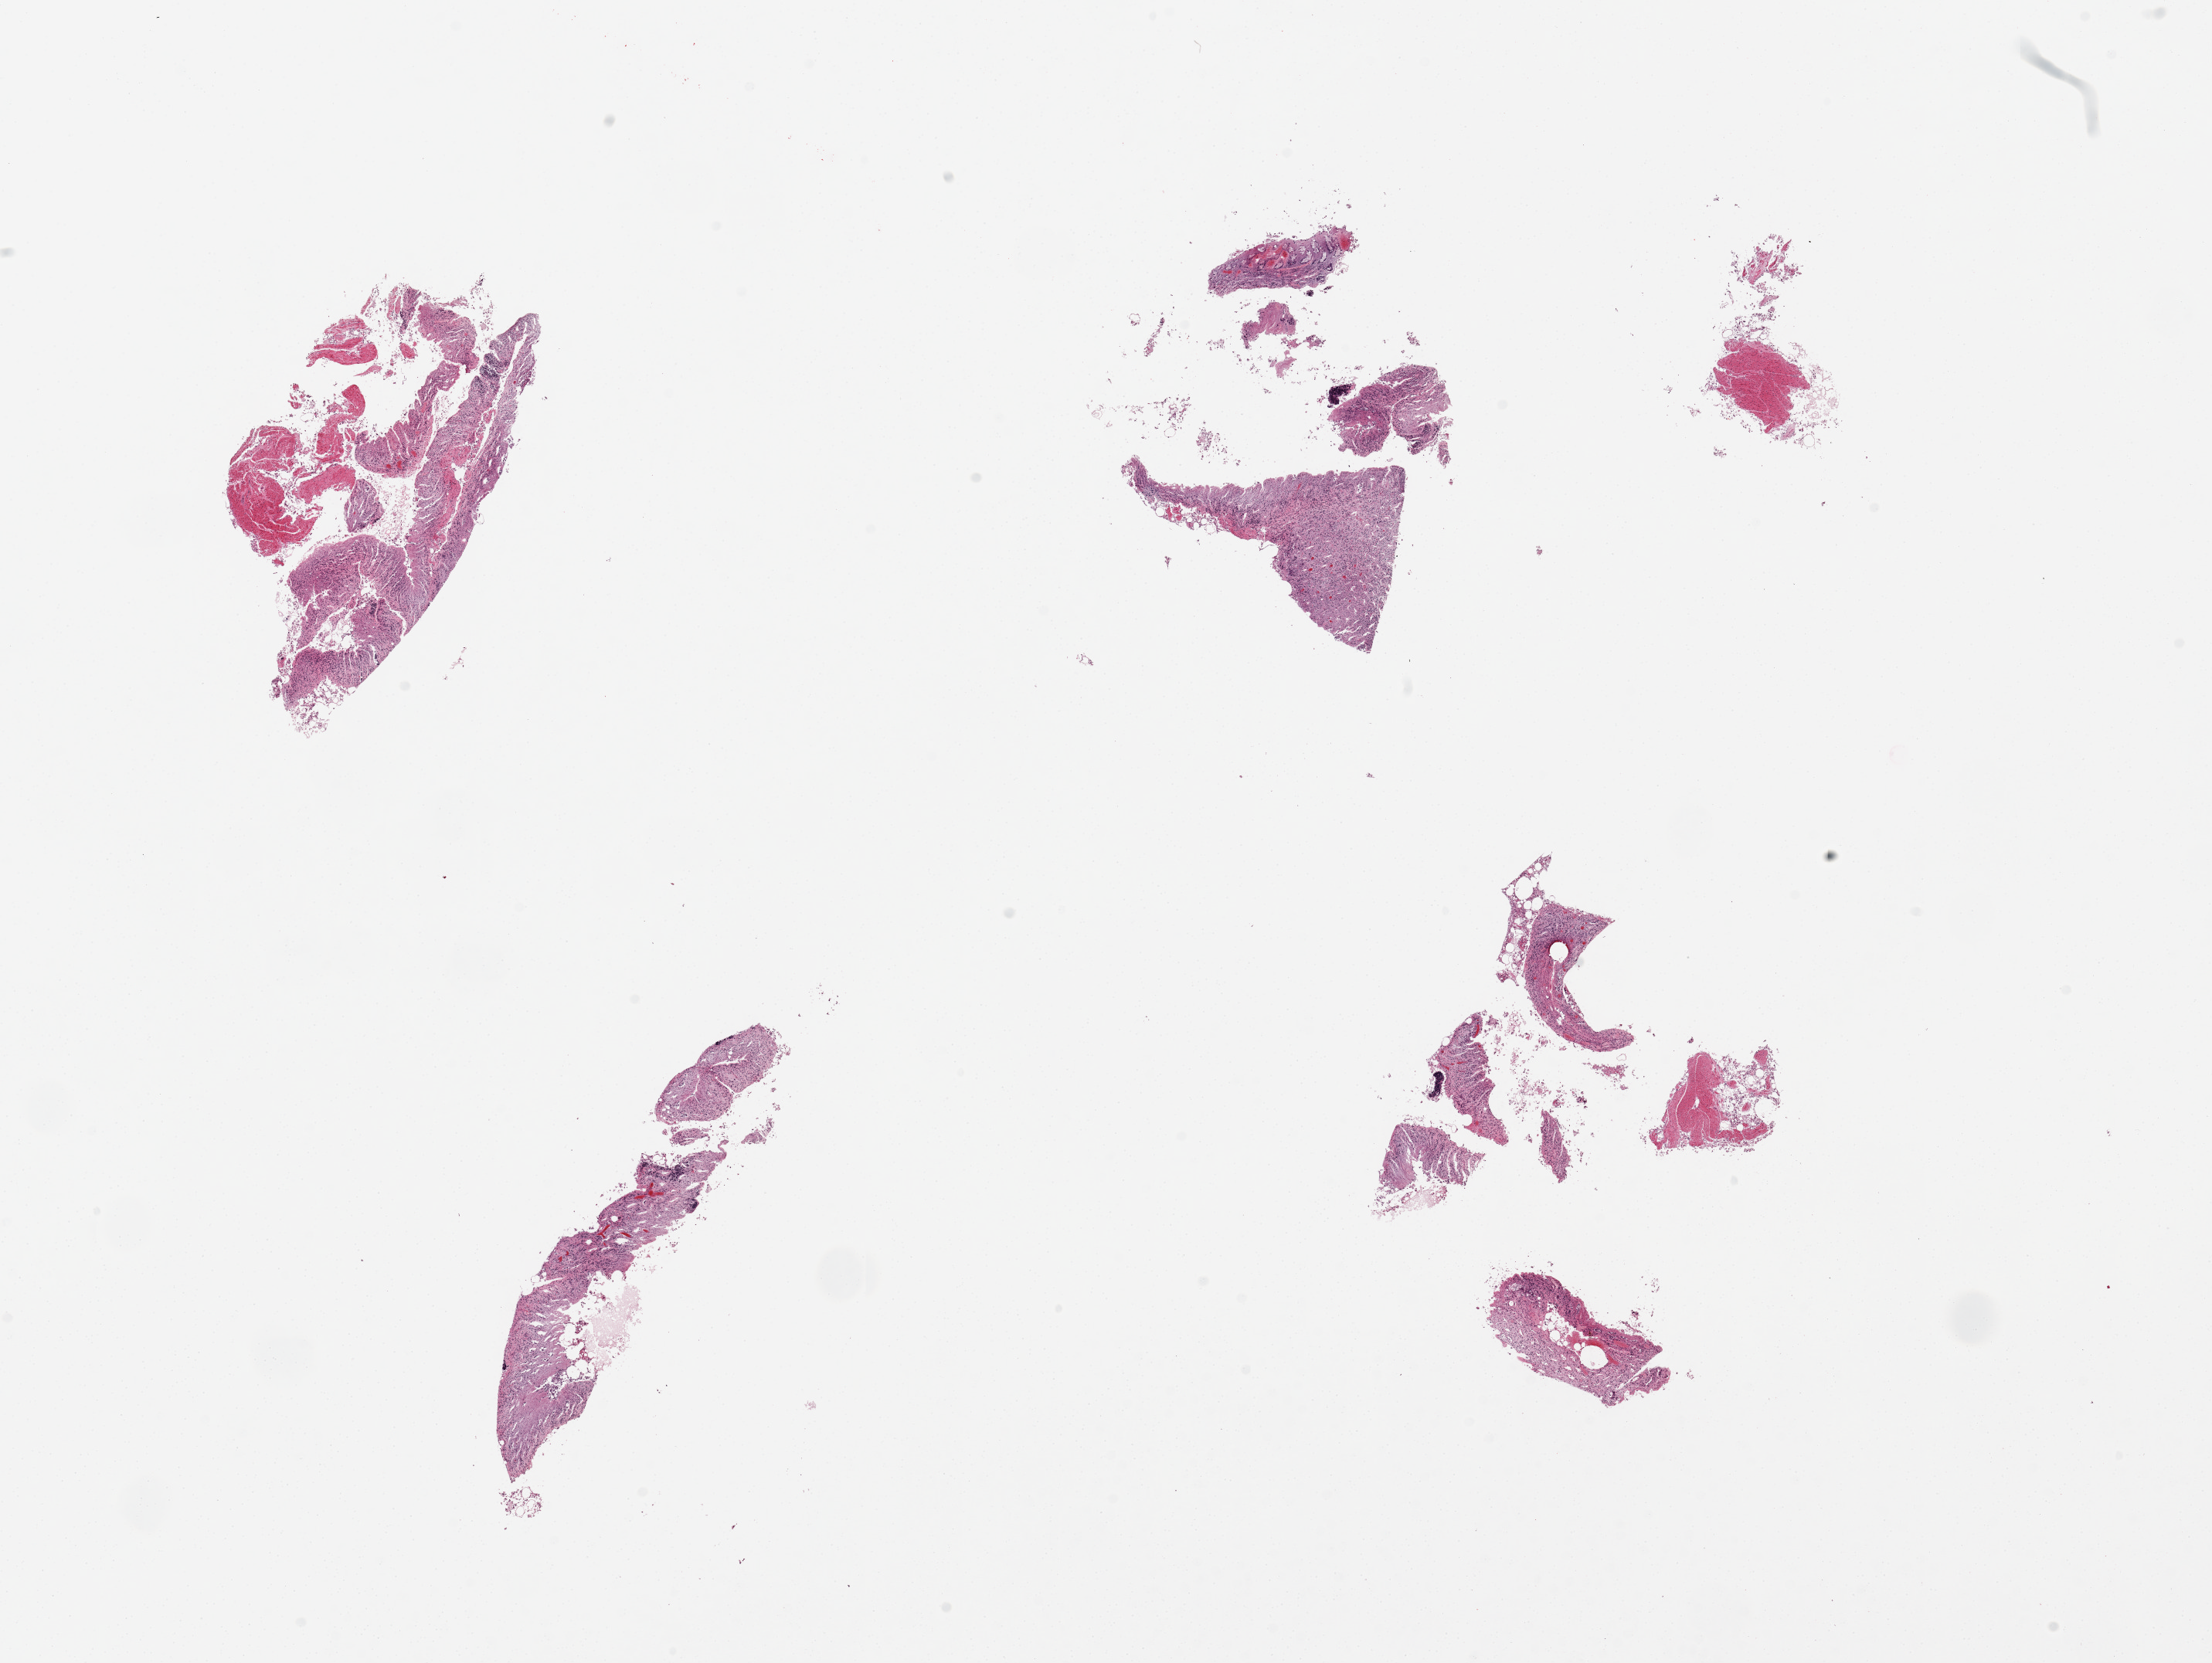
Digitized hematoxylin and eosin (H&E)-stained section, a low-resolution overview of the entire scanned area, about 22.6 x 17.0 mm (acquisition: 20x scan); PAXgene-fixed, paraffin-embedded tissue; target tissue: ileum; donor tissue sample.
Reviewer comment on this tissue sample: multiple dispersed fragments of mucosa, ~5% lymphoid elements, all badly autolyzed.